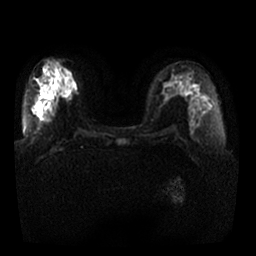
Breast MRI, one axial slice; position 10 of 25 along the scan axis; diffusion-weighted series; image 2 of 4 stored at this slice position (different b-values; order by instance number); 1.5 T; 4 mm slice thickness; 256 × 256 image matrix, field of view 350 × 350 mm. Female patient.
Structures marked on this image (expert manual segmentation):
- tumour on diffusion-weighted imaging: box from (x=65, y=82) to (x=74, y=93) px